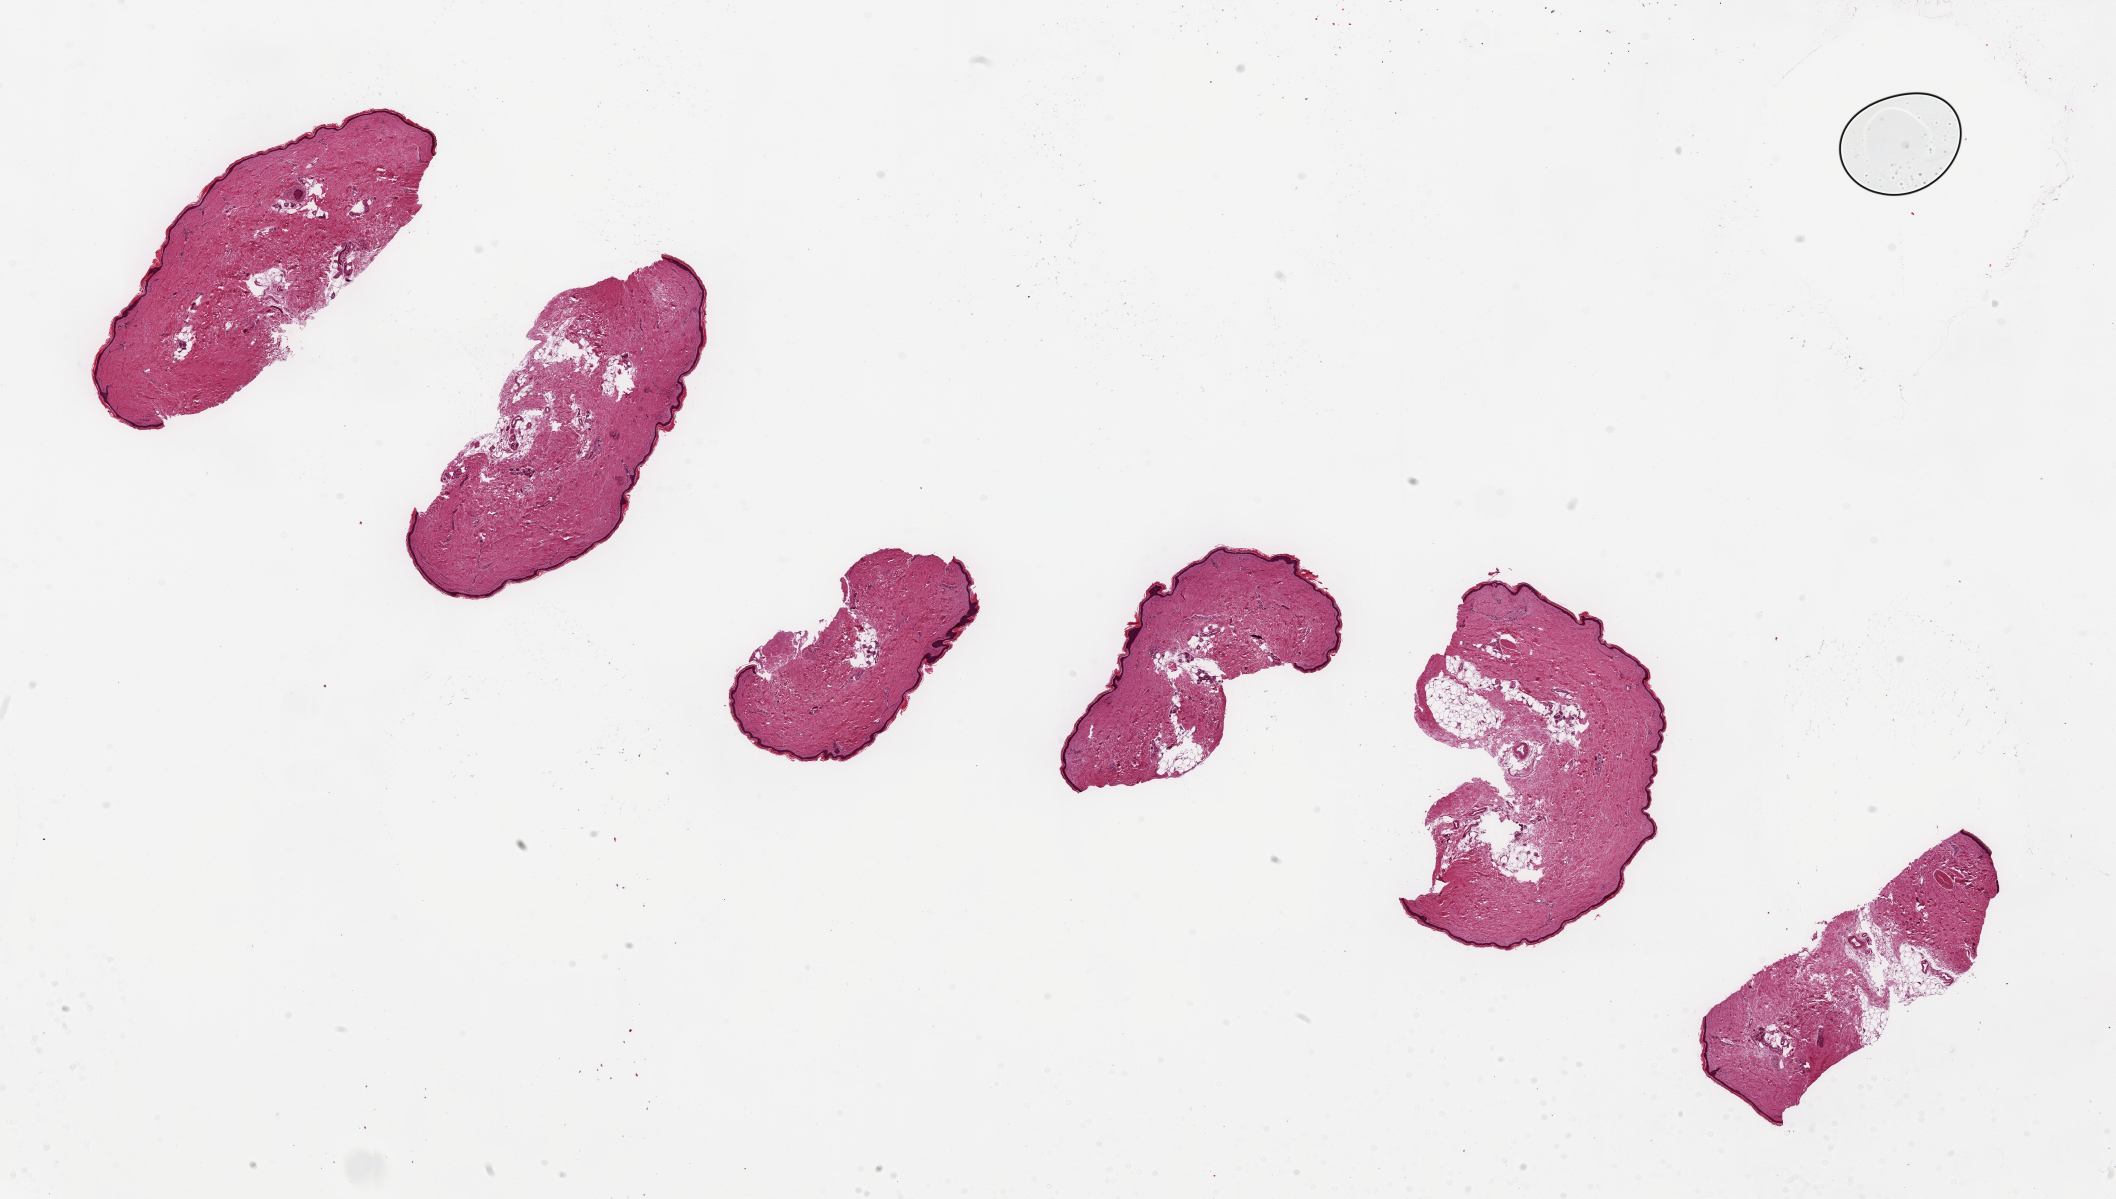
H&E whole-slide image, whole scanned area (about 33.5 x 19.0 mm) shown as a low-resolution overview, PAXgene-fixed, paraffin-embedded tissue, section of skin of lower leg (target tissue), tissue donor sample.
Review note (as recorded): 6 ~5-6x 2.5mm pieces. Squamous epithelium is ~1% of specimen thickness.